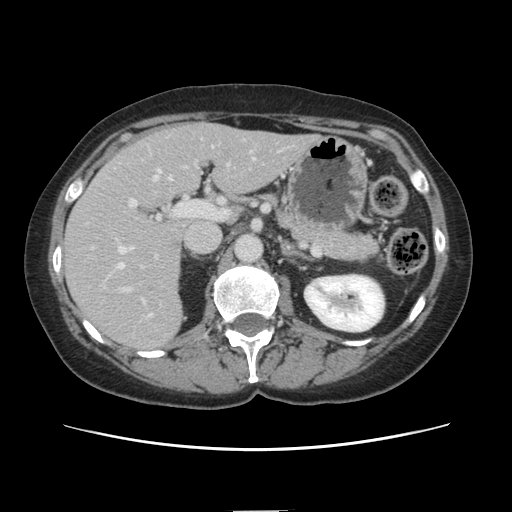
Contrast-enhanced abdominal CT, one axial slice; position 75 of 141 along the scan axis; 120 kVp; soft-tissue window (W 400 / L 40 HU); 2.5 mm slice thickness; 512 × 512 image matrix, field of view 350 × 350 mm. Female patient, age 63 years. Case-level facts recorded for this patient, not image findings: diagnosis: colorectal cancer liver metastases, imaged before liver resection; multiple liver metastases: yes; largest metastasis: 3.2 cm; disease in both lobes: yes.
Structures marked on this image (outlined manually by an expert reader):
- hepatic veins: bounding box [x1, y1, x2, y2] px = [116, 170, 171, 270]
- liver: [66, 124, 312, 352]
- planned liver remnant (the part of the liver to remain after resection): [175, 124, 313, 195]
- portal vein (with intrahepatic branches): [122, 180, 212, 316]